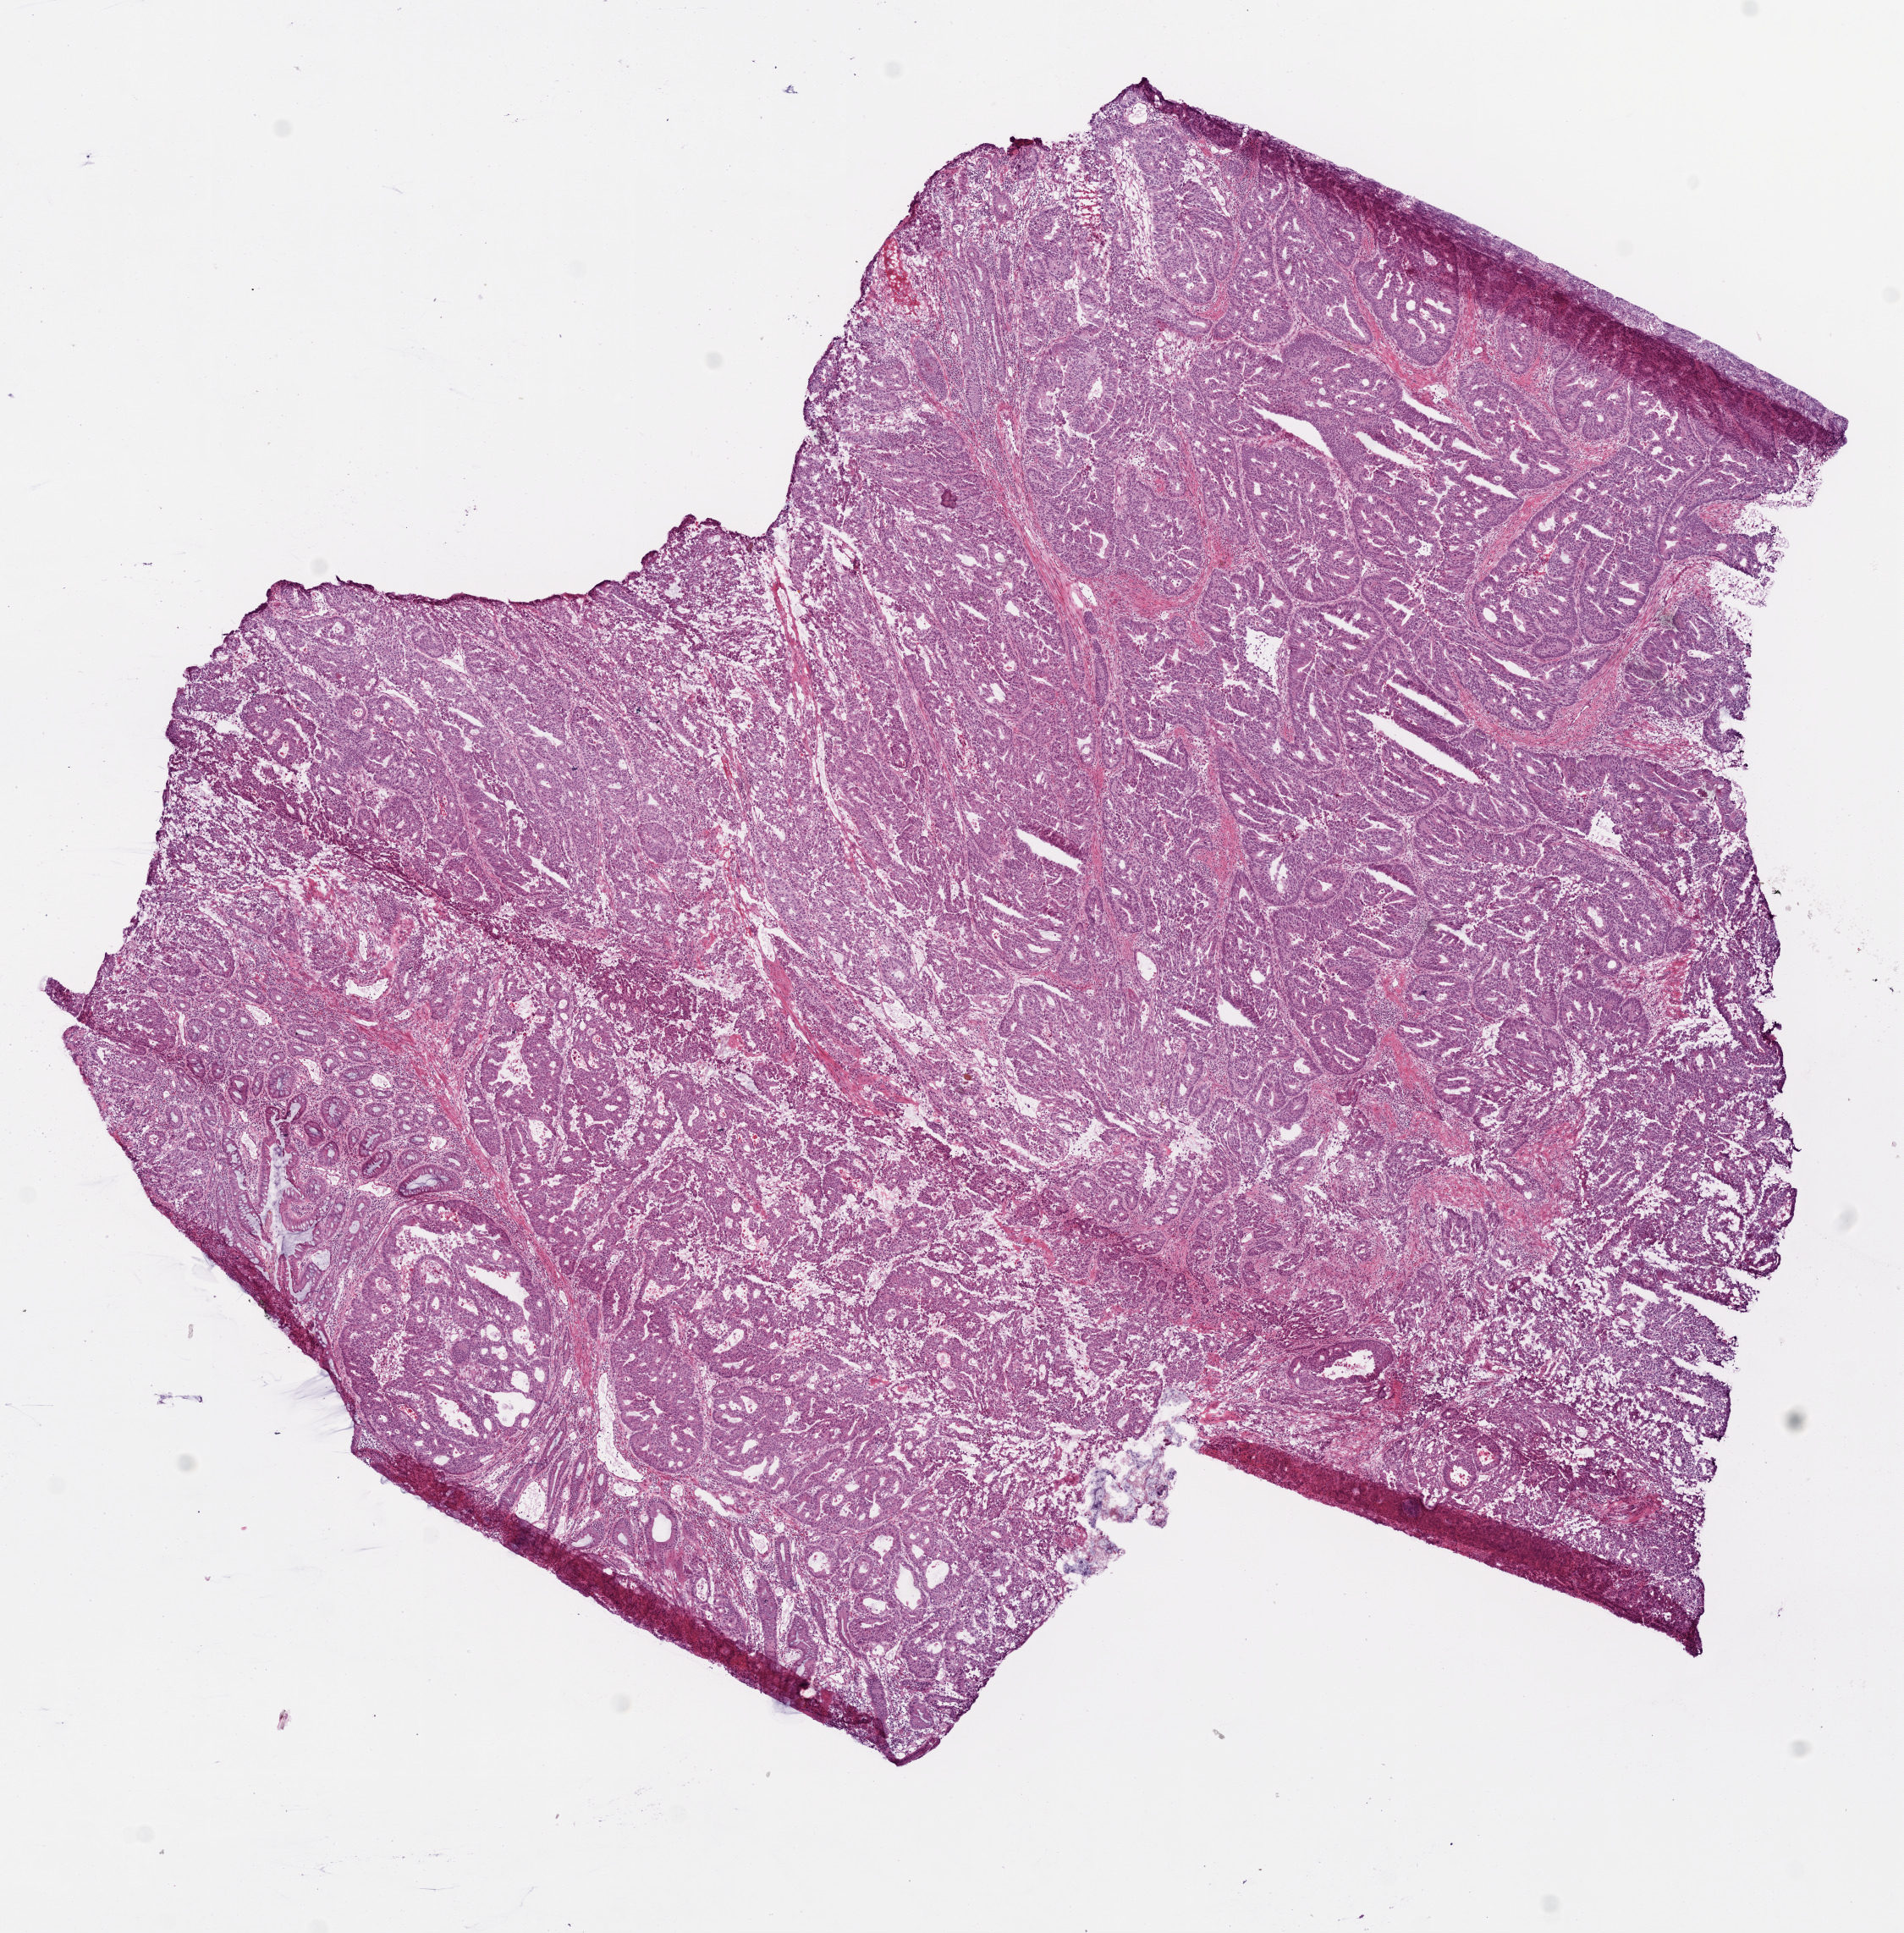
Digitized Hematoxylin and eosin (H&E) stained tissue section (whole slide), shown as a low-resolution overview of the whole scanned area (about 9.0 x 9.2 mm, slide scanned at 20x), frozen section from the top of the tissue portion, sample: primary tumour, colon. Female, age 82 years at initial diagnosis. Composition of this section per pathologist review: tumour cells 82%, tumour nuclei 85%, normal cells 0%, stromal cells 10%, necrosis 8%.
Histologic diagnosis: Adenocarcinoma, NOS (sigmoid colon). Lymph nodes positive (case pathology): 6 of 12 examined. TNM: T3 N2 M0. AJCC pathologic stage: IIIC (6th edition).